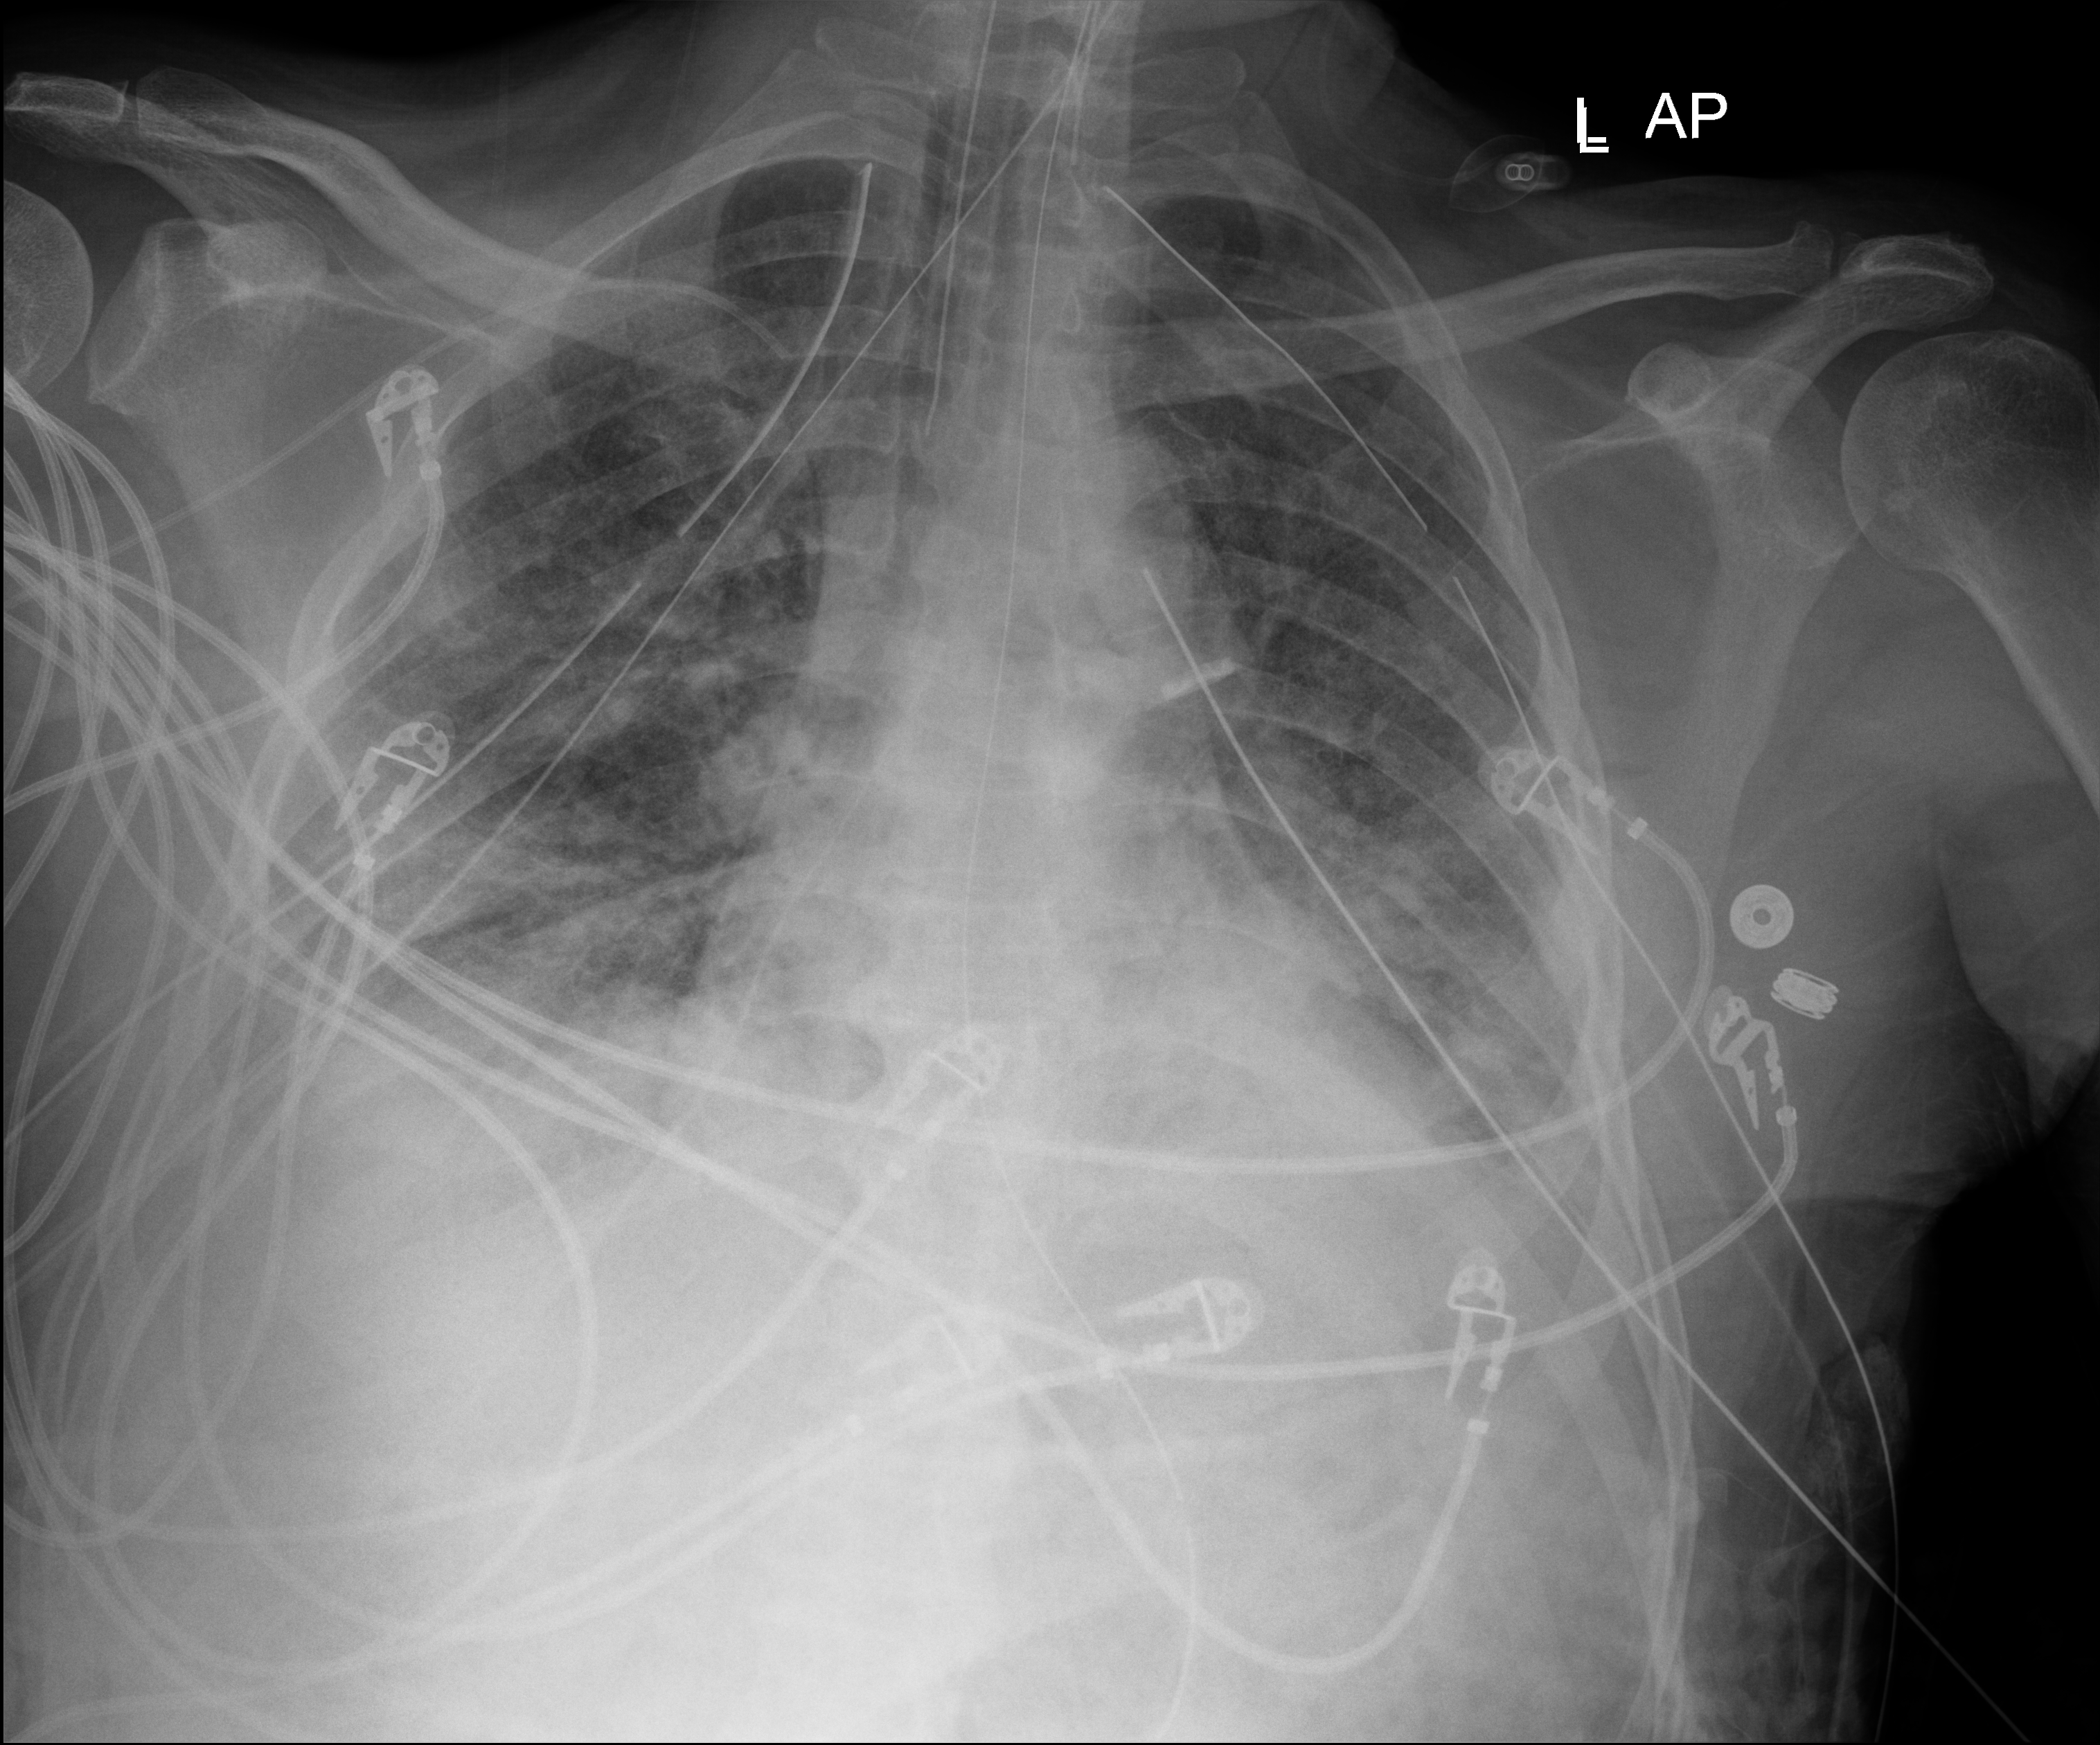
Chest X-ray (portable); anteroposterior (AP) projection. Male patient hospitalised with COVID-19, age 18–59 years.
Admission-level facts for this patient (not findings on this image; timing relative to this image not recorded): admitted to intensive care during this hospital stay: yes; diabetes (admission record): no.